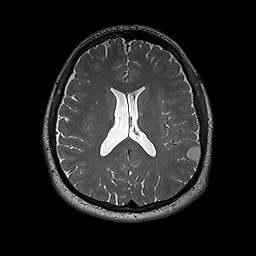
Brain MRI from a brain-tumour surgery series, one axial slice; slice 85 of 192 in the series (ordered by position); 1 mm slice thickness; 256 × 256 image matrix, field of view 250 × 250 mm. From the clinical record (not read from this slice): histopathology: Dysembryoplastic neuroepithelial tumor; WHO grade: 1; IDH mutation: no.
Annotated regions visible in this slice (outlined manually by an expert reader):
- tumour: bounding box [x1, y1, x2, y2] px = [187, 147, 201, 163]